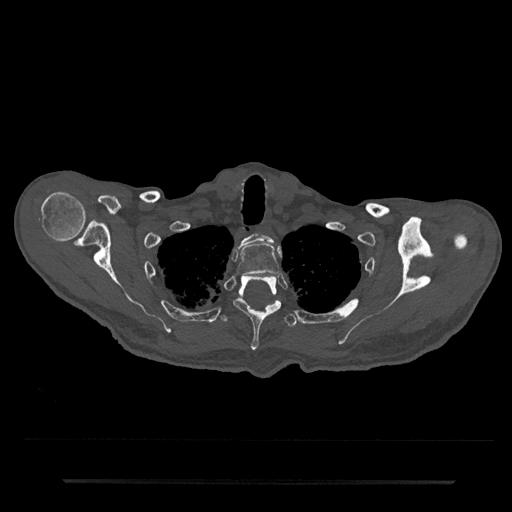
CT including the spine, one axial slice; position 664 of 797 along the scan axis; reconstruction kernel Br40s/3; 120 kVp; bone window (W 1800 / L 400 HU); 0.5 mm slice thickness; 512 × 512 image matrix. Male patient, age 74 years. From the clinical record (not read from this slice): primary cancer: prostate.
Annotated regions visible in this slice (semi-automatically segmented with operator editing):
- T1 vertebra: box from (x=240, y=233) to (x=274, y=246) px
- T2 vertebra: (x=236, y=243)–(x=279, y=276)
- T3 vertebra: (x=233, y=275)–(x=282, y=351)
- T4 vertebra: (x=218, y=301)–(x=298, y=328)